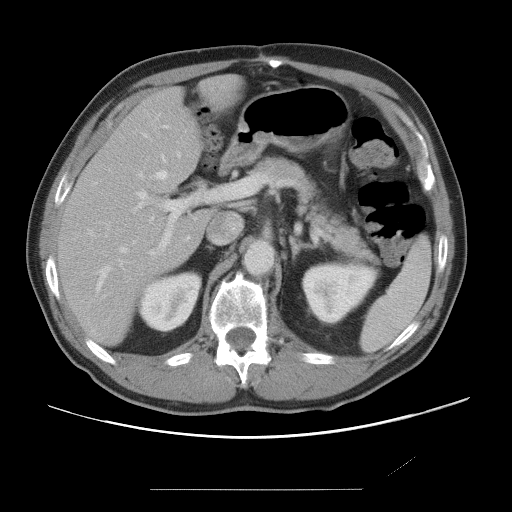
Contrast-enhanced abdominal CT, one axial slice. Slice 42 of 87 in the series (ordered by position). Intravenous contrast given. Soft-tissue window (W 400 / L 40 HU). 5 mm slice thickness. 512 × 512 image matrix, field of view 406 × 406 mm. Male patient, age 74 years. From the clinical record (not read from this slice): diagnosis: colorectal cancer liver metastases, imaged before liver resection.
Structures marked on this image (manually delineated by an expert):
- hepatic veins: box from (x=96, y=133) to (x=181, y=291) px
- liver: (x=58, y=77)–(x=240, y=346)
- planned liver remnant (the part of the liver to remain after resection): (x=58, y=77)–(x=243, y=345)
- portal vein (with intrahepatic branches): (x=137, y=173)–(x=273, y=256)